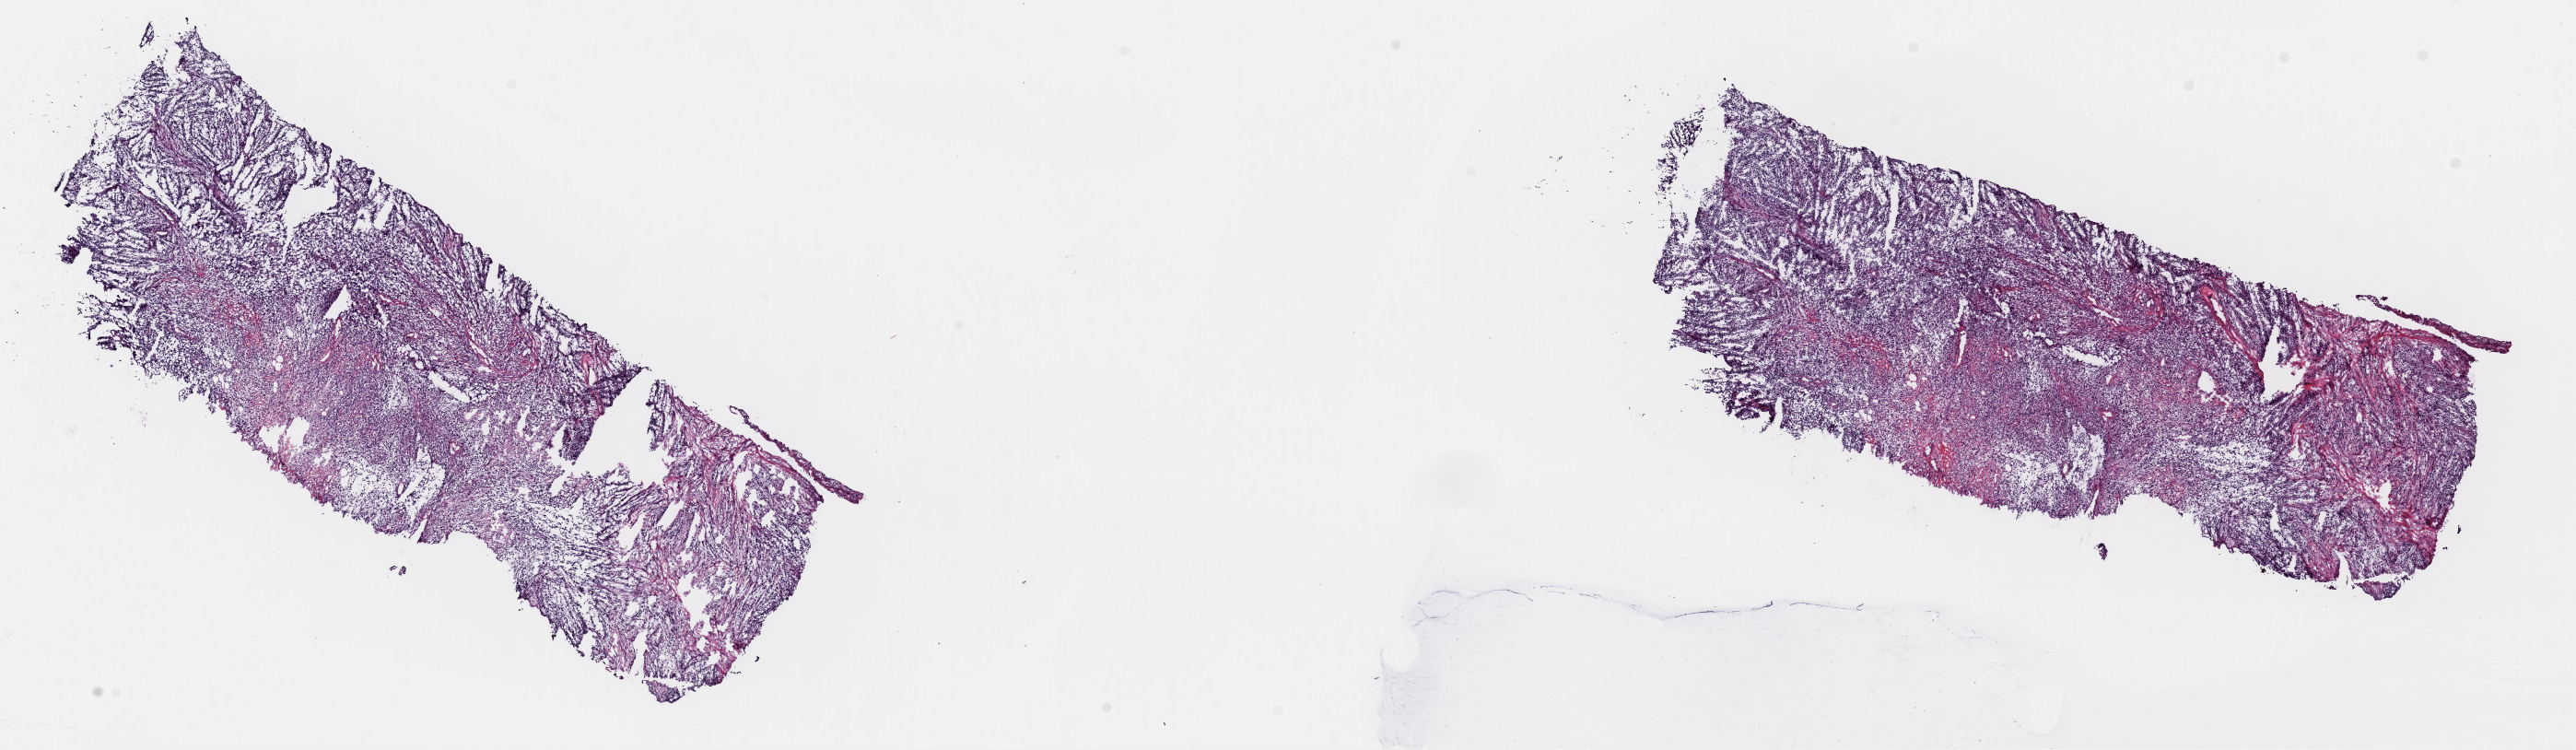
Digitized Hematoxylin and eosin (H&E) stained tissue section (whole slide), shown as a low-resolution overview of the whole scanned area (about 22.1 x 6.4 mm, acquisition: 40x scan); frozen section from the top of the tissue portion; metastatic tumour sample, sampled site: lymph node. Male patient; age at initial diagnosis 63 years. Slide review estimates, as recorded: tumour cells 90%, tumour nuclei 80%, normal cells 0%, stromal cells 7%, necrosis 3%. Infiltration values recorded for this section: lymphocyte infiltration 8%, monocyte infiltration 5%, neutrophil infiltration 0%.
This section: metastatic tumour tissue. Patient diagnosis: Malignant melanoma, NOS.